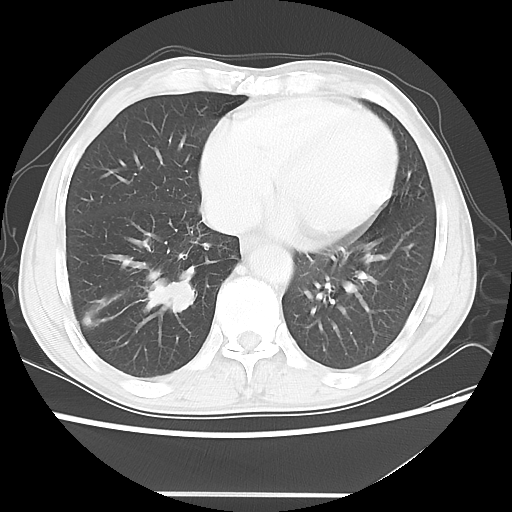
Chest CT, one axial slice; slice 17 of 56 in the series (ordered by position); 120 kVp; lung window (W 1500 / L -600 HU); 5 mm slice thickness; 512 × 512 image matrix. Male patient, age 65 years. From the clinical record (not read from this slice): clinical TNM (as recorded): T1c N3 M0; histopathological grade: G3.
Structures marked on this image (bounding box drawn by a radiologist):
- lung tumour (recorded histology: small cell carcinoma): bounding box [x1, y1, x2, y2] px = [142, 266, 204, 315]